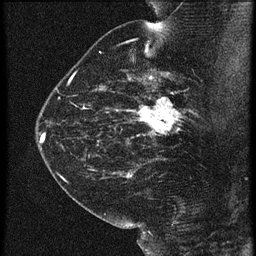
Breast MRI (dynamic contrast-enhanced), one sagittal slice; position 40 of 60 along the scan axis; 3 images stored at this slice position (order not interpretable as contrast timing); 1.5 T; TE 4.2 ms, TR 21.3 ms; 1.5 mm slice thickness; 256 × 256 image matrix. Female patient, age 42 years. Case-level facts recorded for this patient, not image findings: setting: breast cancer imaged before/during neoadjuvant chemotherapy; receptor status: HER2-positive.
Annotated regions visible in this slice (semi-automatically segmented with operator editing):
- analysis volume of interest (the breast-tissue region the enhancement analysis was run in; not a lesion): bounding box (x1, y1, x2, y2) in pixels: (122, 82, 195, 147)
- tumour enhancement mask (voxels above the 90 % enhancement threshold inside the analysis volume of interest): (133, 98, 186, 135)